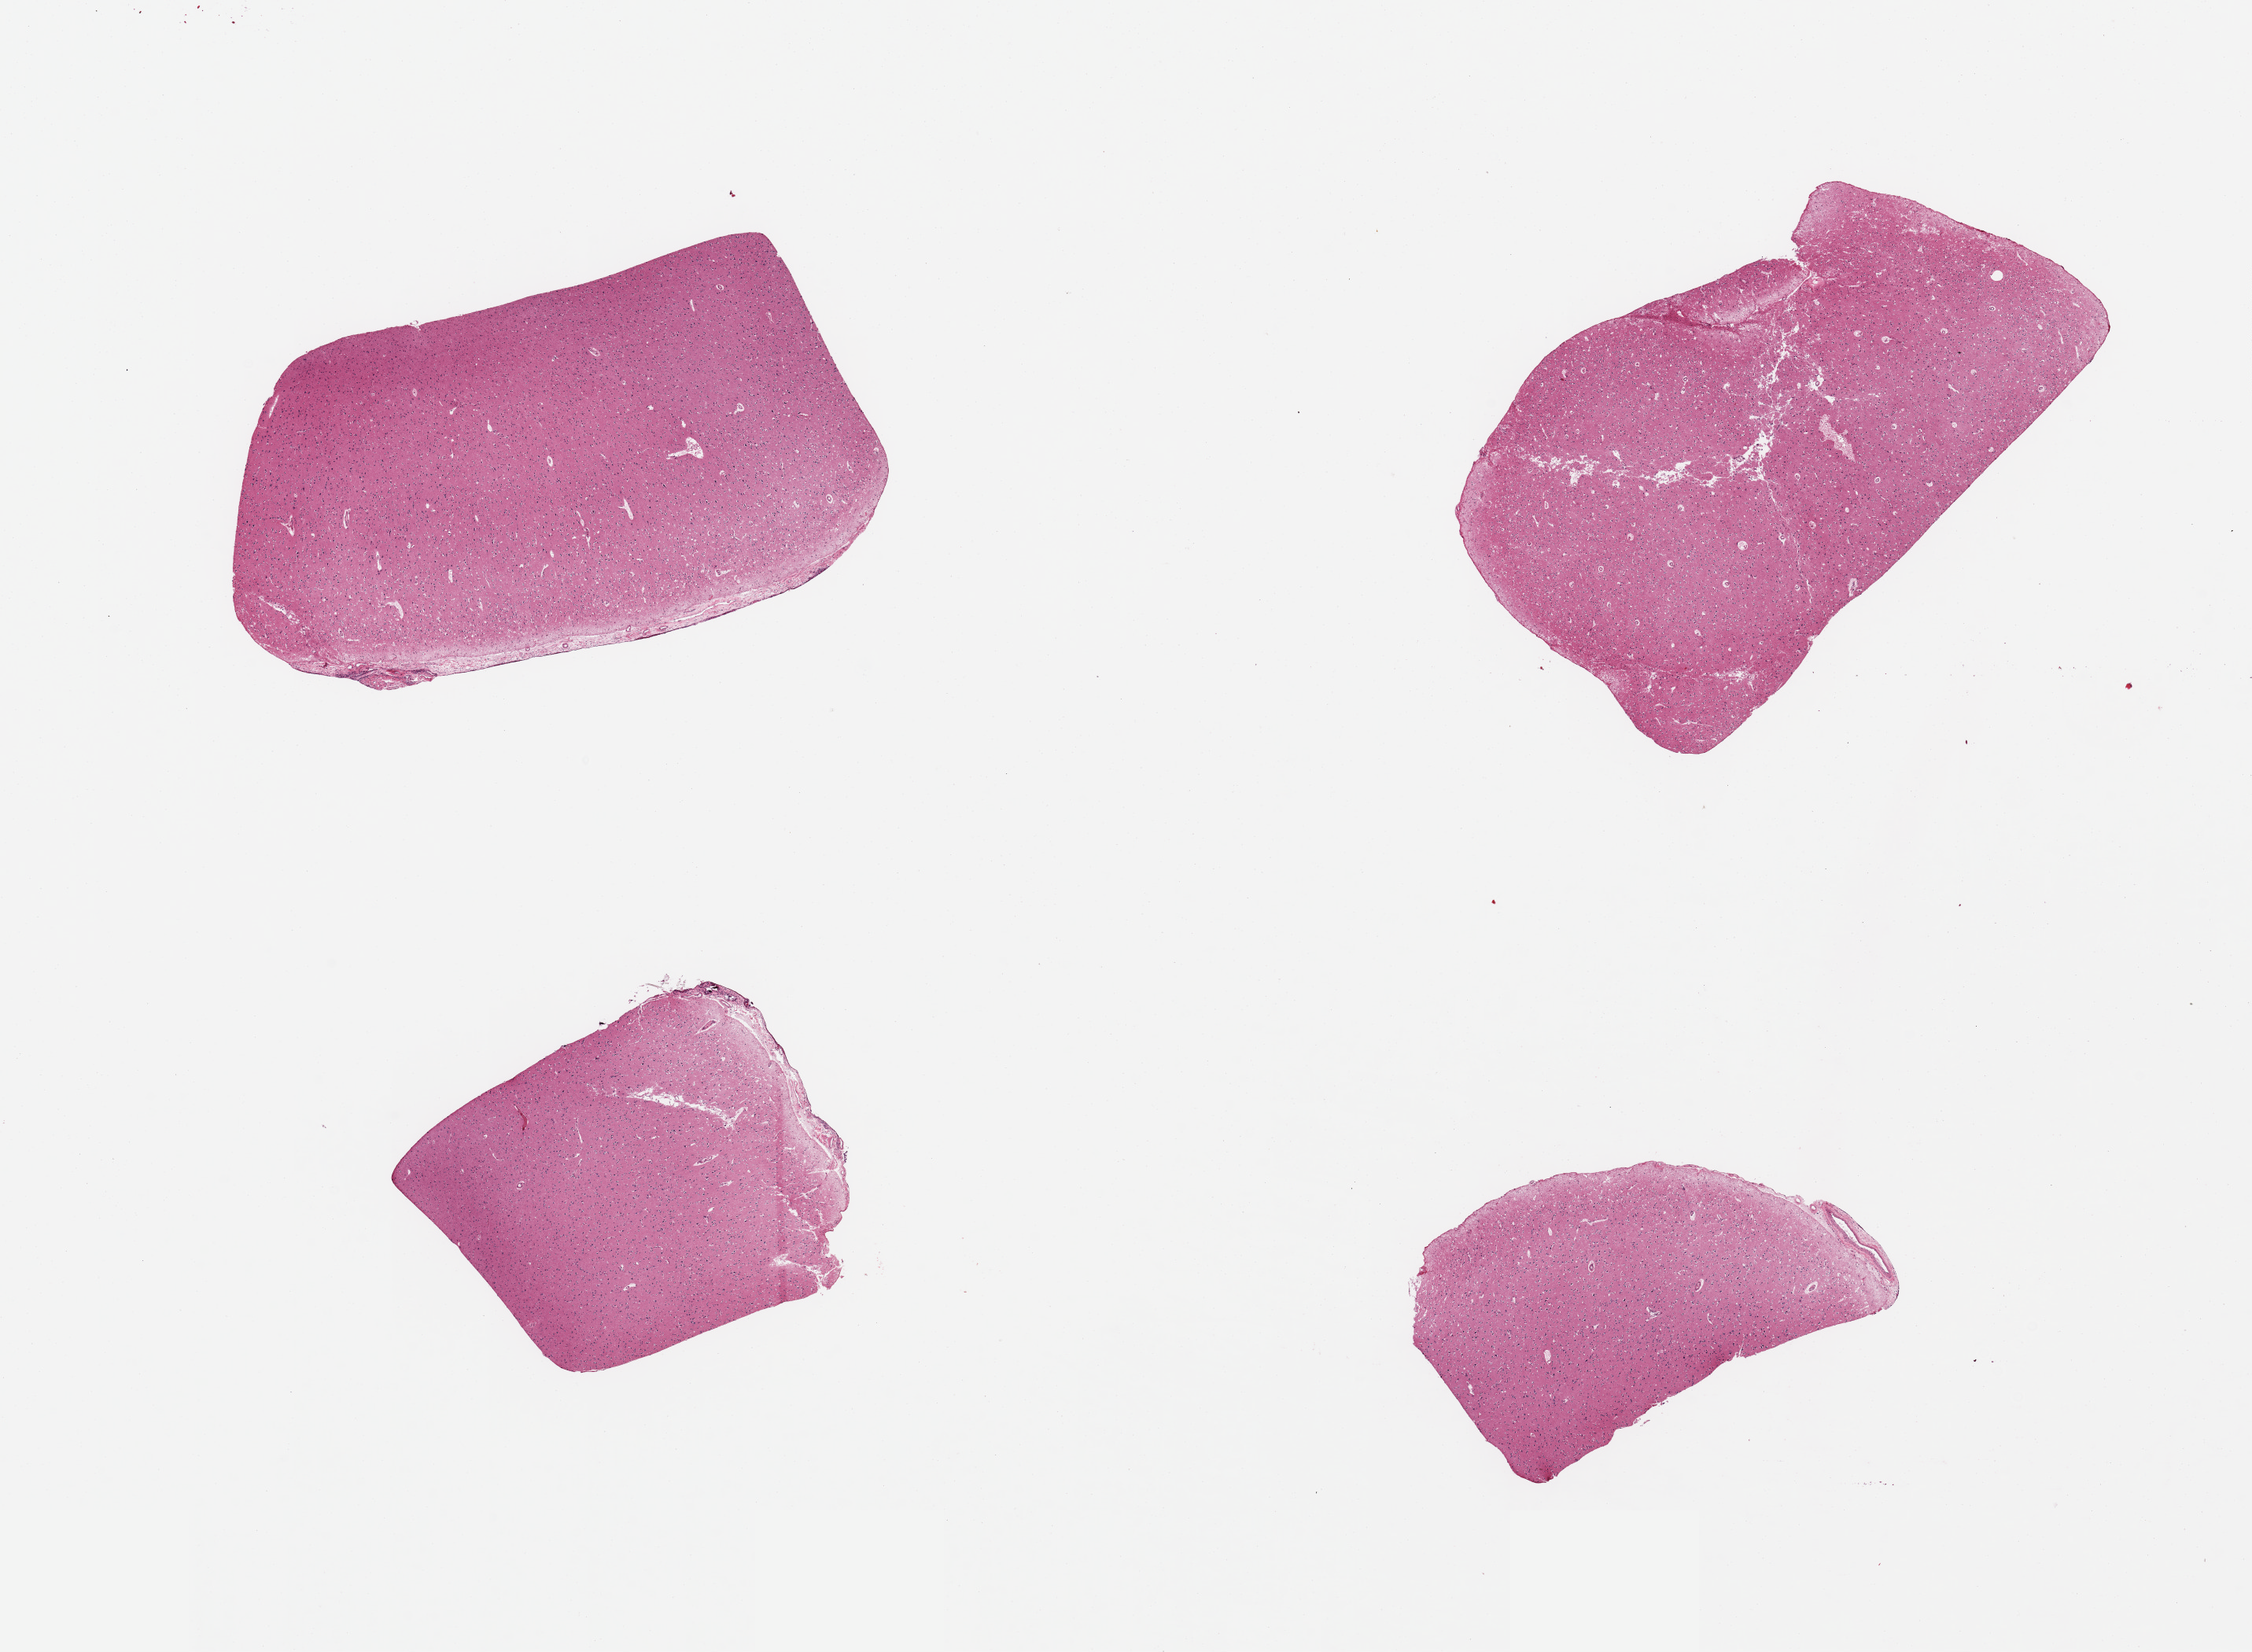
Whole-slide image, hematoxylin and eosin (H&E) stain — shown as a low-resolution overview of the whole scanned area (about 22.6 x 16.6 mm). PAXgene-fixed paraffin-embedded (PFPE) section. Target tissue: cerebral cortex. Donor tissue sample. Donor sex: male.
- review note (as recorded): 4 pieces, no abnormalities